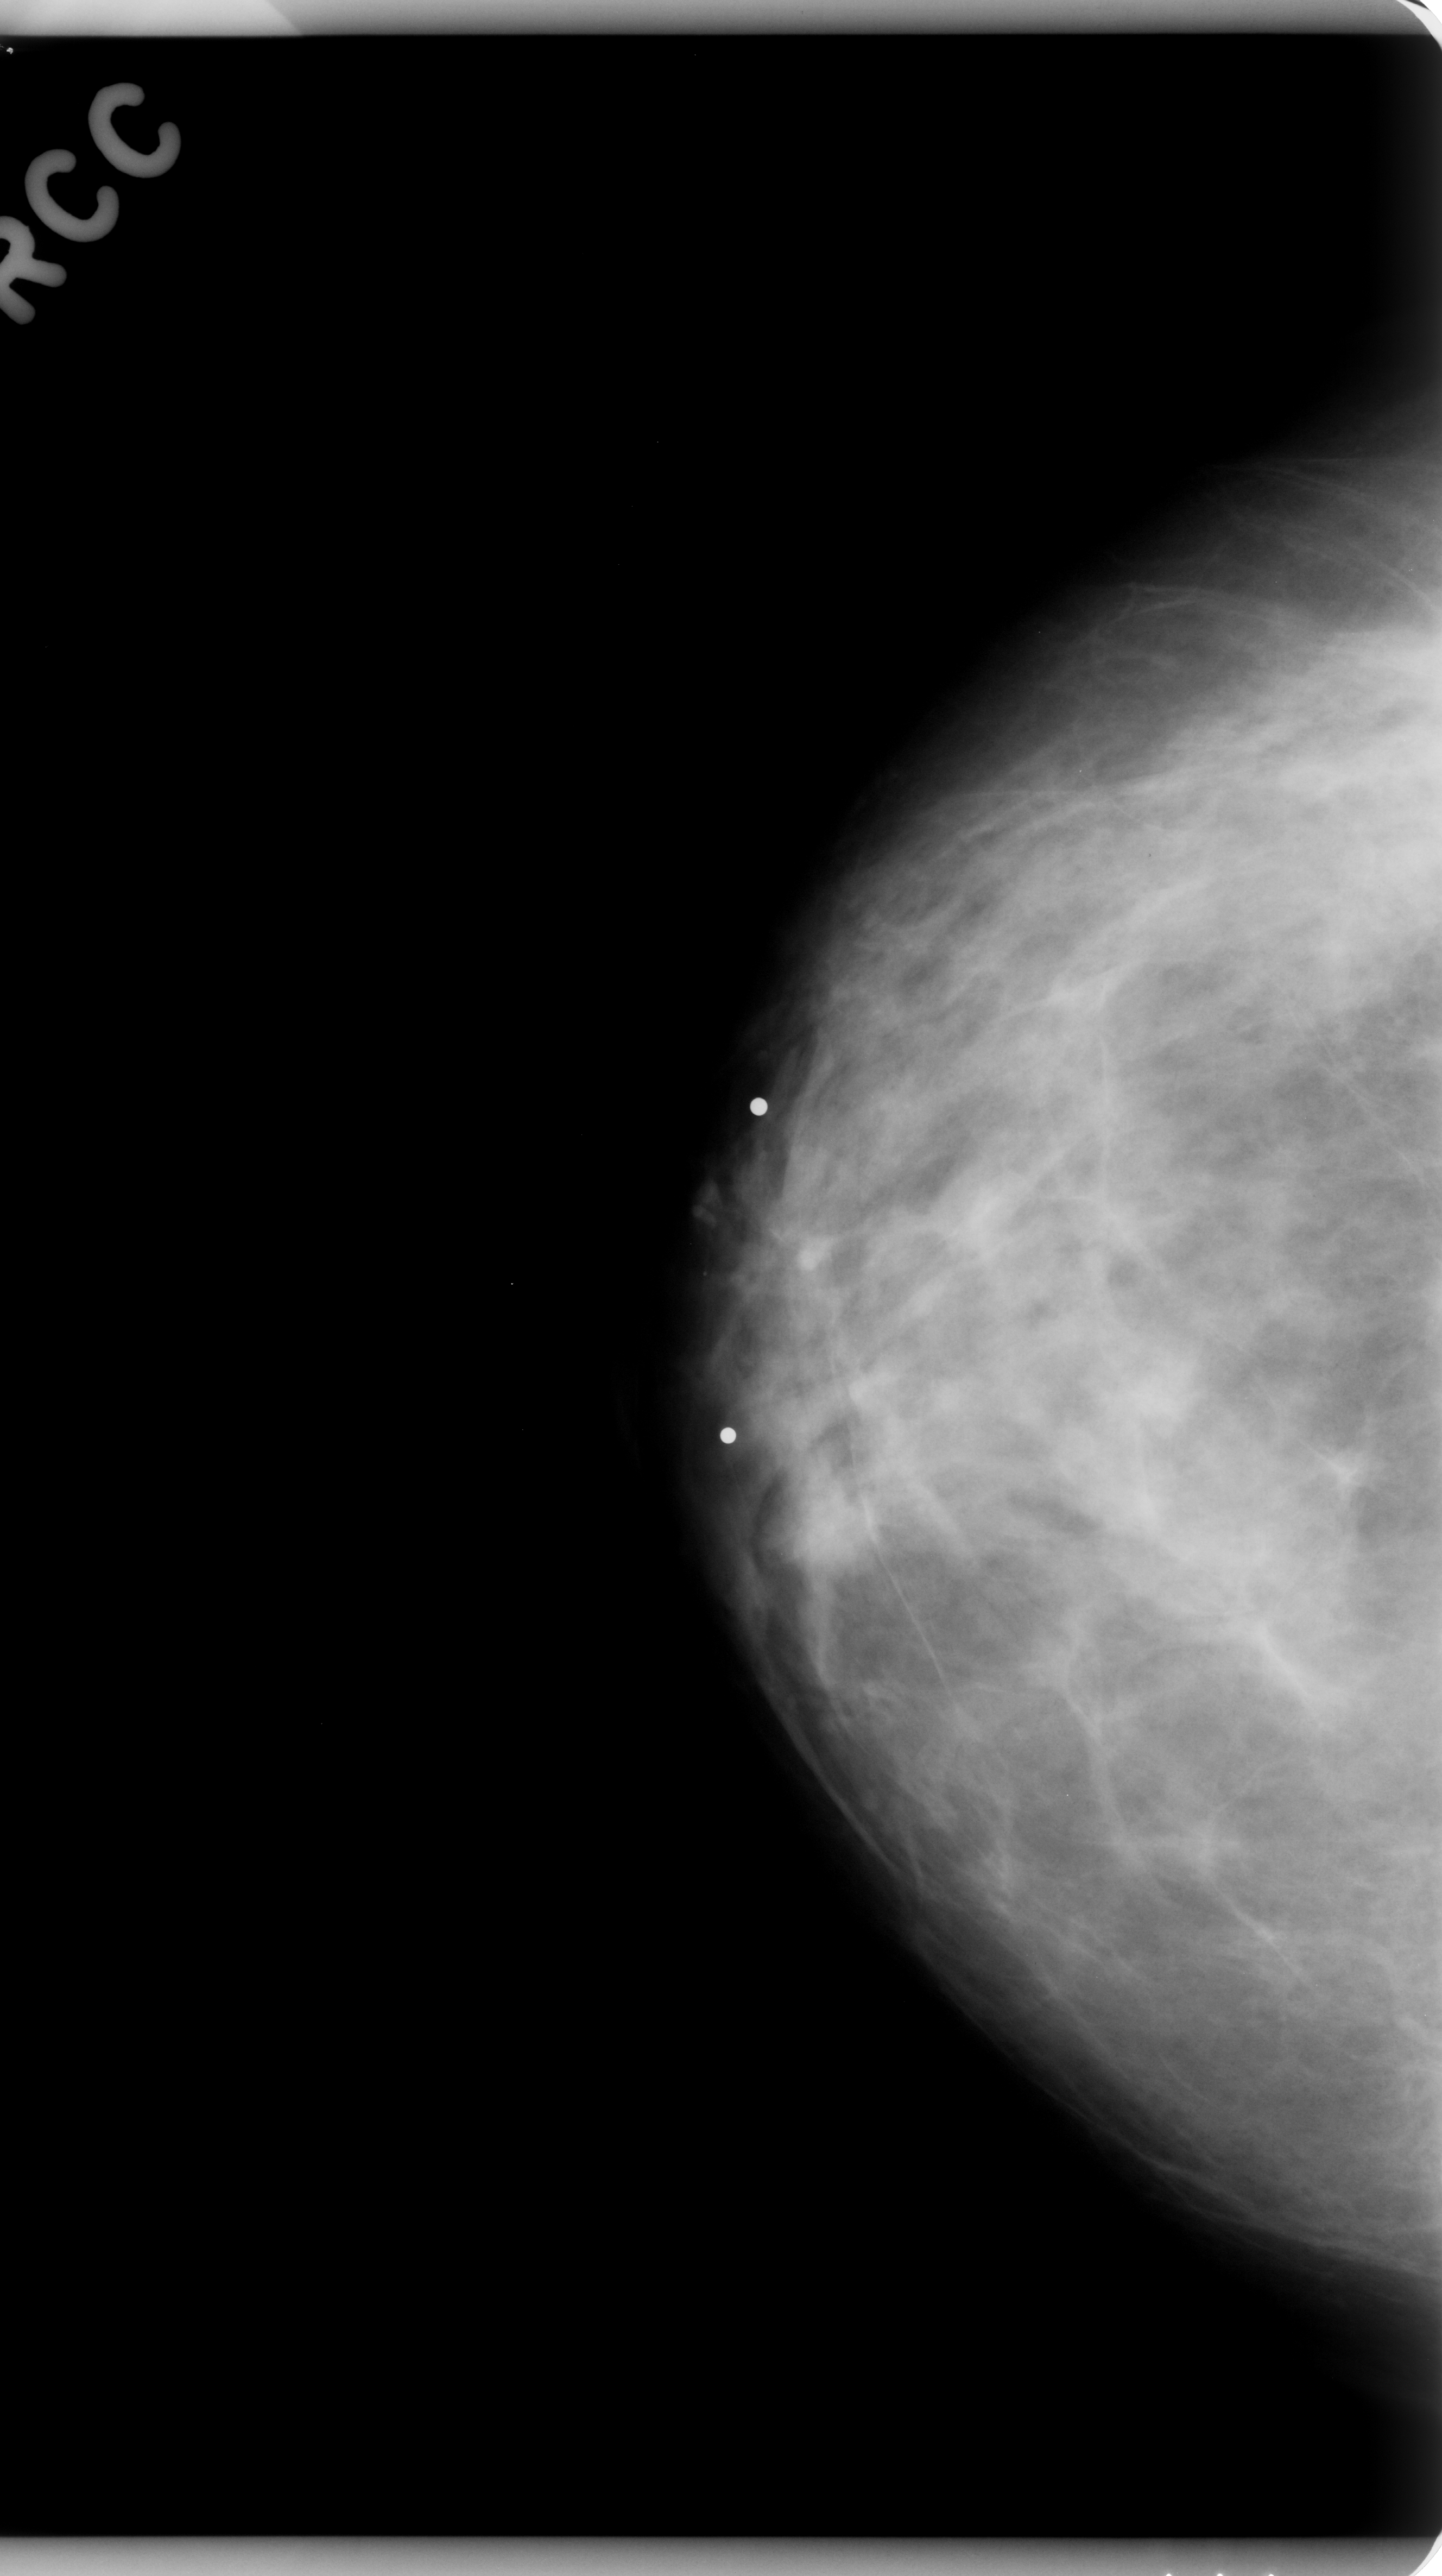
Scanned film-screen mammogram. Right breast. Craniocaudal (CC) view. BI-RADS breast density category 2 (scale 1–4). 1442 × 2576 image matrix.
Expert-marked regions of interest on this image (one box per marked abnormality):
- mass, shape oval, margins microlobulated; BI-RADS assessment category 4; subtlety rating 4 on a 1 (subtle) to 5 (obvious) scale; pathology (as recorded): benign: bounding box (x1, y1, x2, y2) in pixels: (765, 1449, 893, 1592)